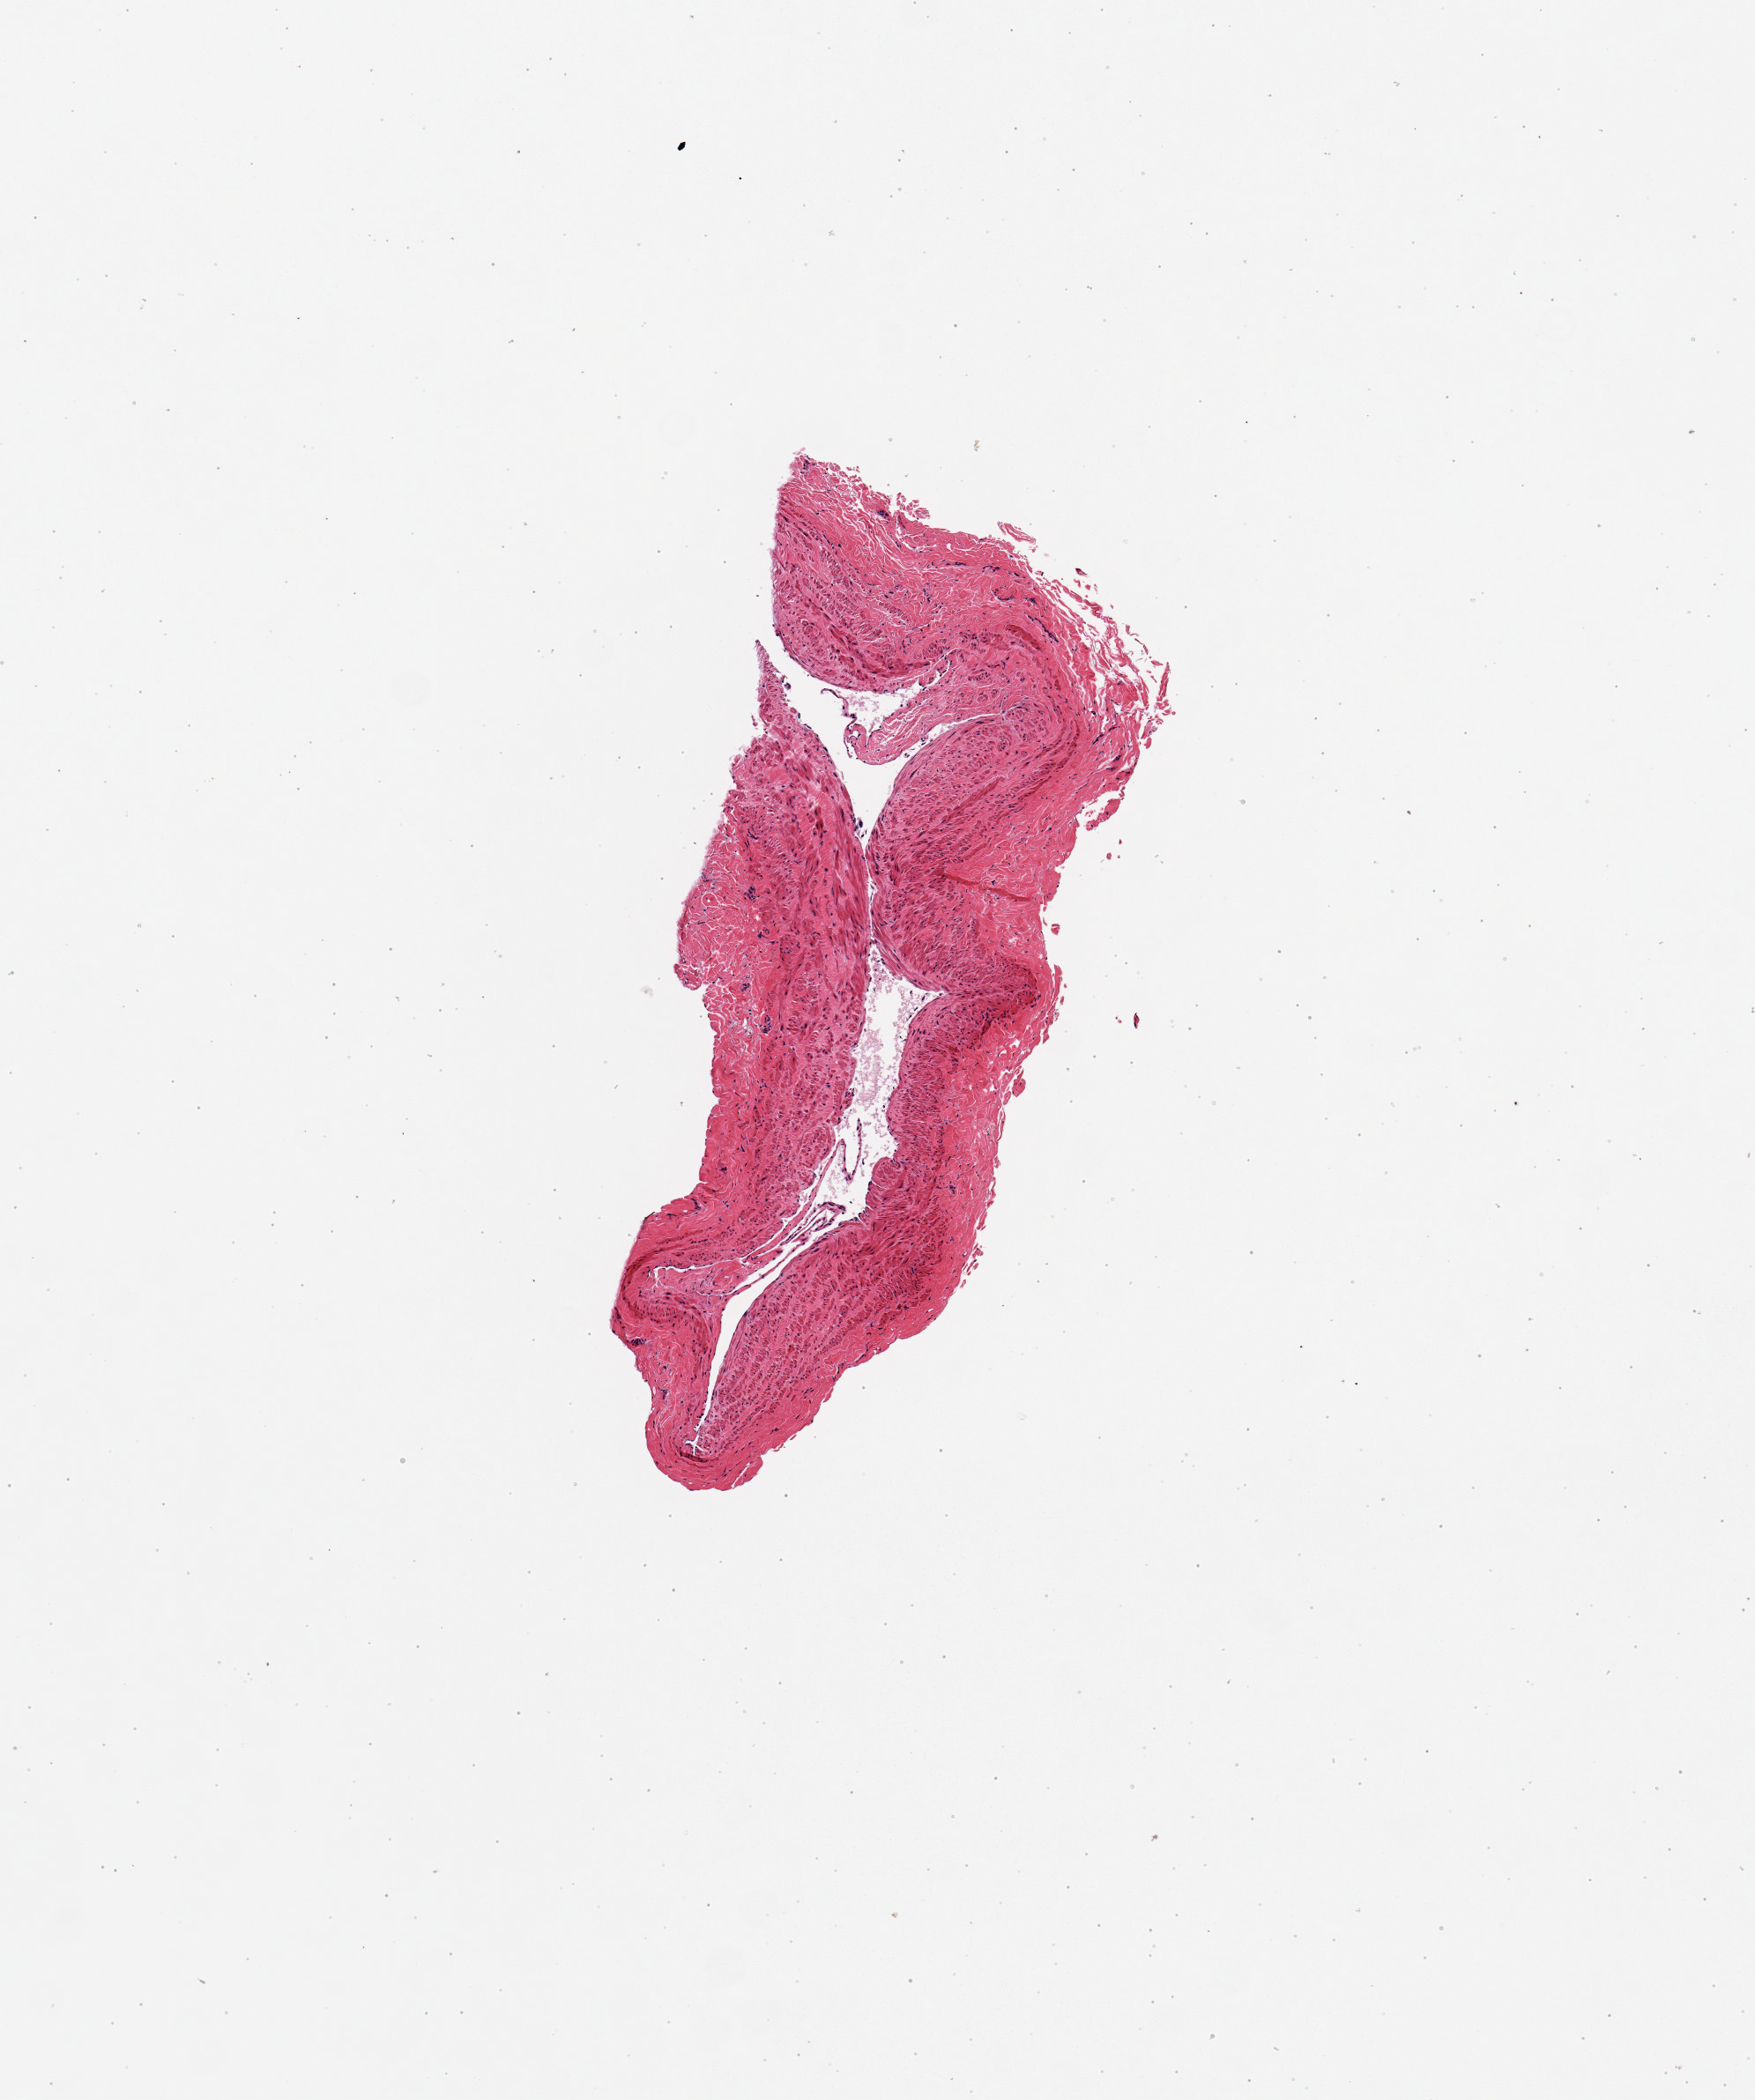
Hematoxylin and eosin (H&E) whole-slide image, low-resolution overview of the scanned area, about 3.9 x 4.7 mm; PAXgene-fixed paraffin-embedded (PFPE) section; section of tibial artery (target tissue); tissue donor sample. Donor sex: male.
* reviewer comment on this tissue sample: 1 piece; well trimmed